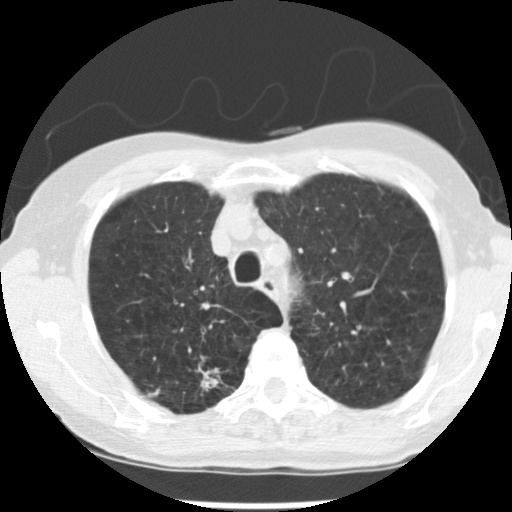
Low-dose screening chest CT, axial slice; baseline screening round; lung window (W 1500 / L -600 HU); 2.5 mm slice thickness; 120 kVp; slice 55 of 265 in the series. Female participant, aged 72 years at enrolment. Current smoker at enrolment.
• Lesion marked by an expert reader, bounding box <183,354,238,406> (left, top, right, bottom; pixels).
• The screening reader recorded 3 non-calcified nodules or masses ≥4 mm on this exam; which of them this box marks is not recorded.
• Official screen result: positive, change unspecified: nodule(s) >= 4 mm or enlarging nodule(s), mass(es), or other non-specific abnormalities suspicious for lung cancer.